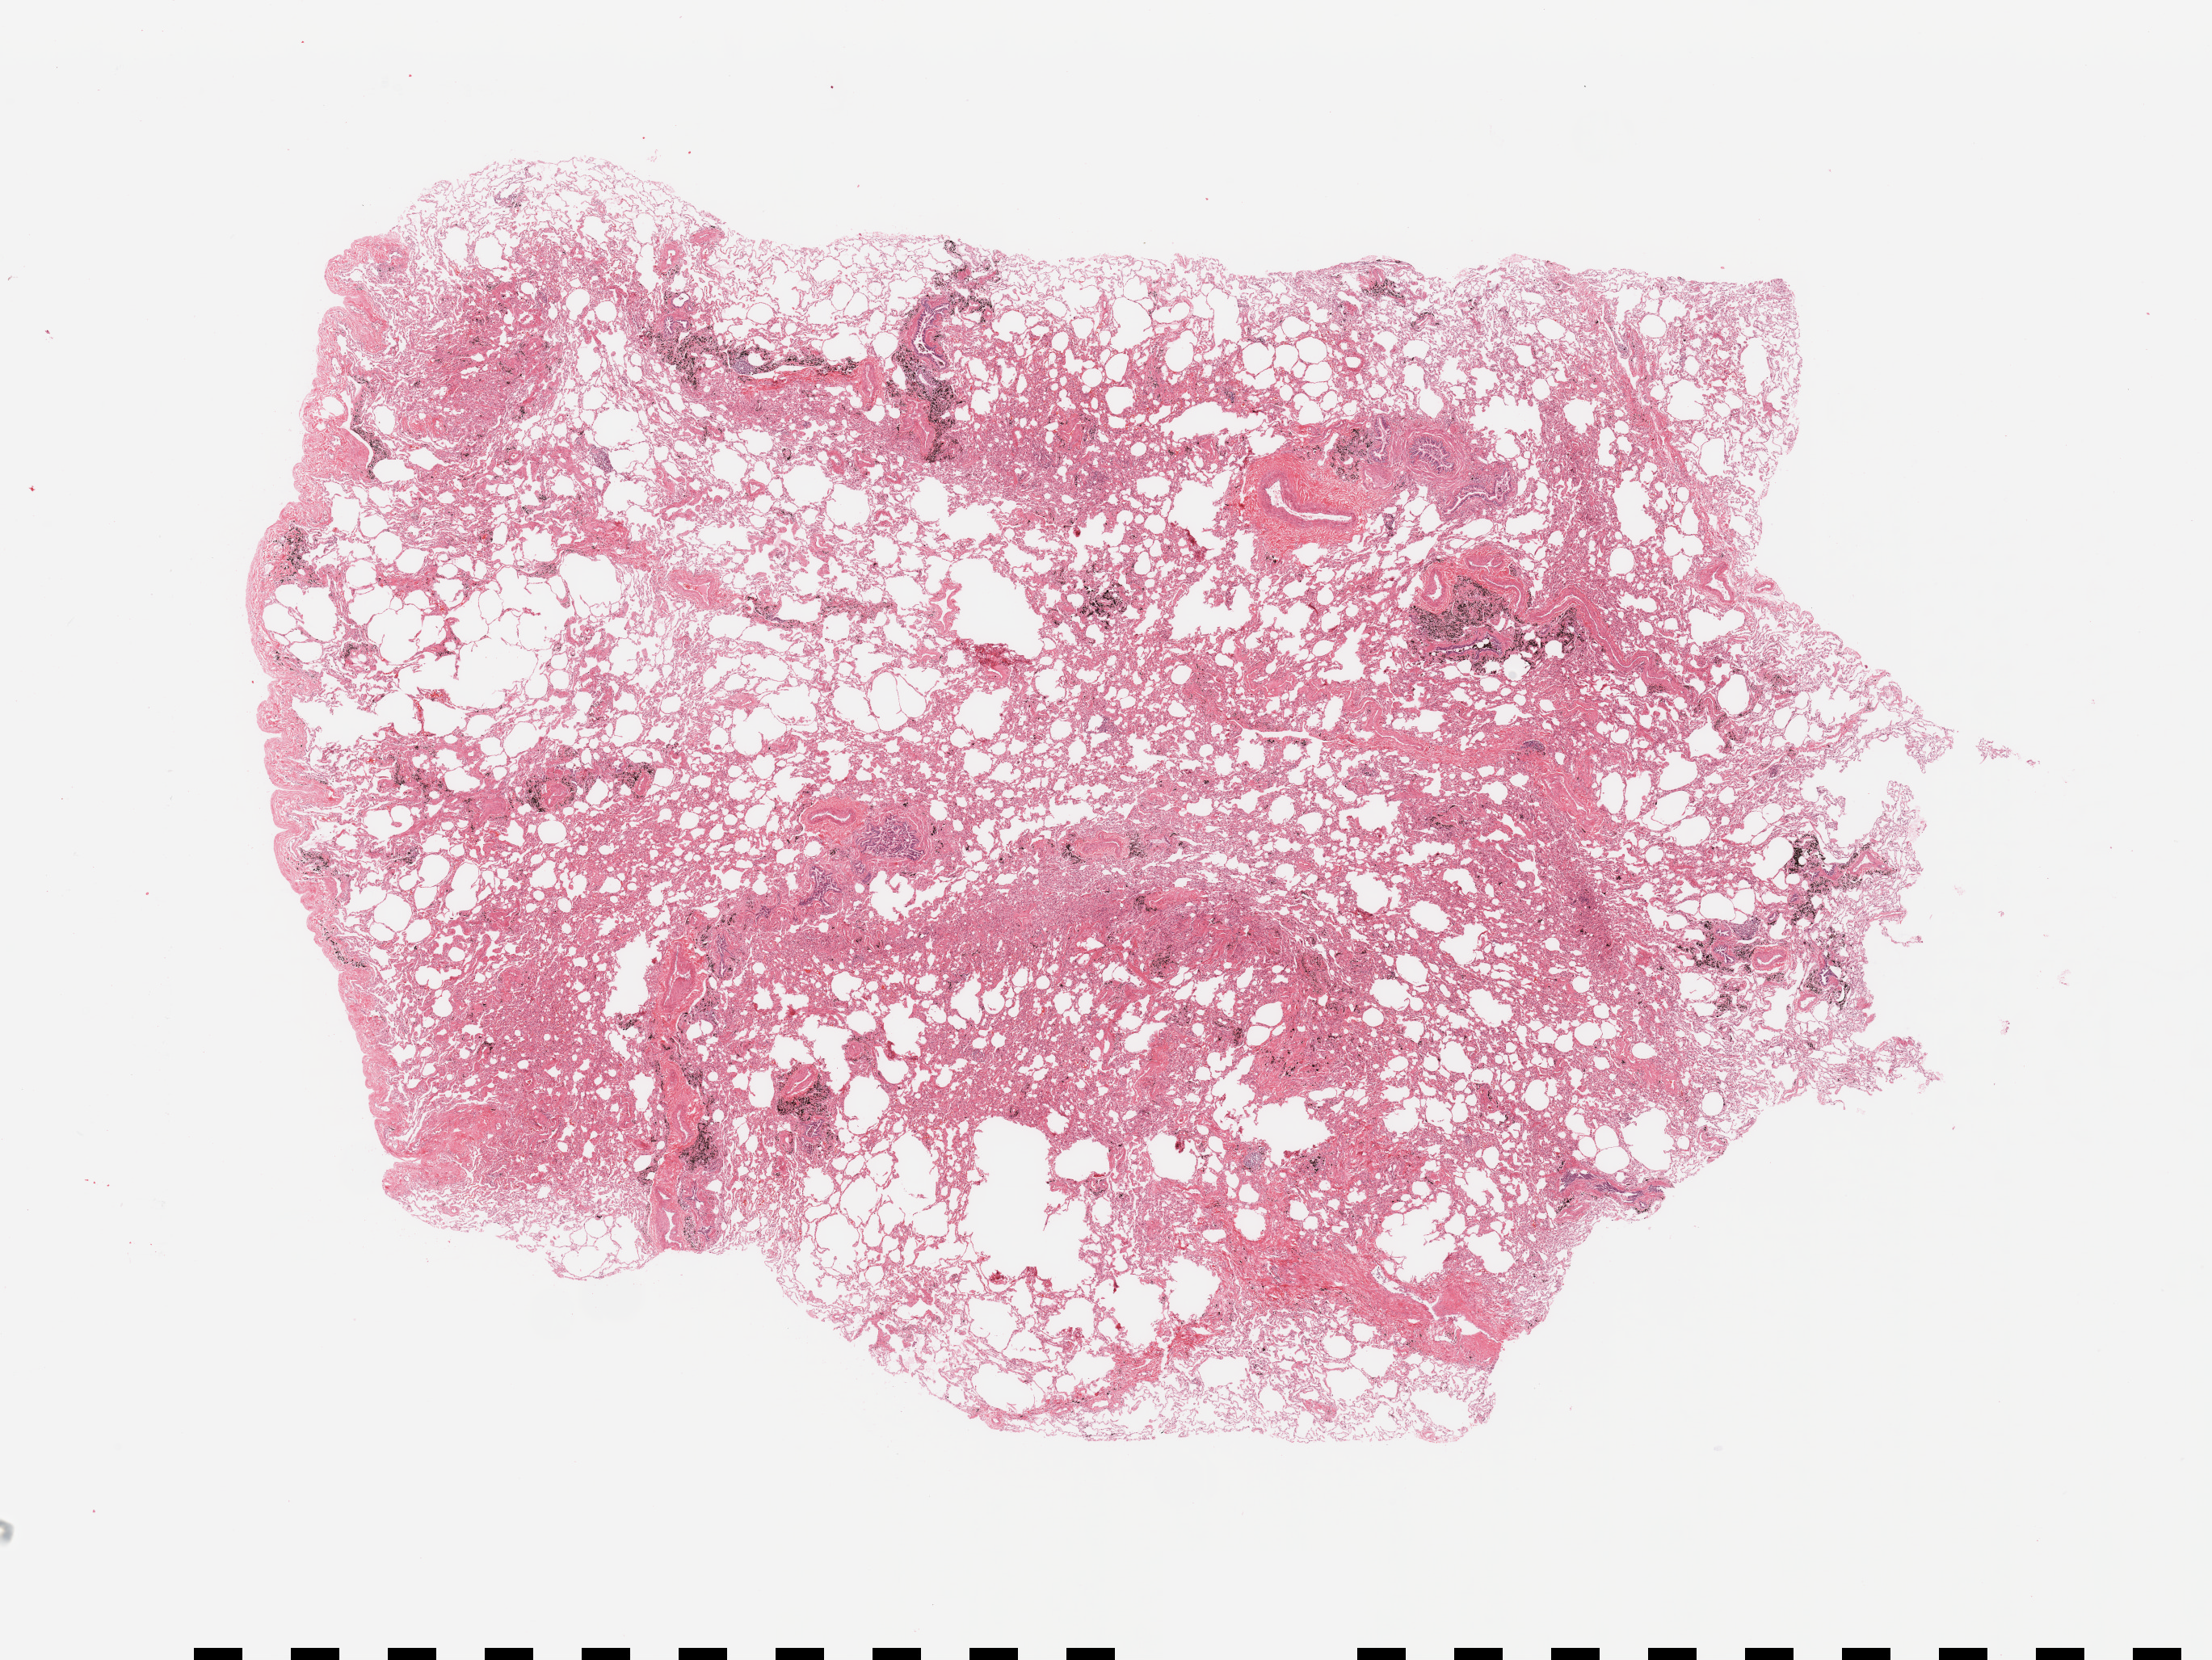
H&E whole-slide image — low-resolution overview of the scanned area, about 21.7 x 16.3 mm. Normal (non-tumour) tissue sample, sampled site: lung. Female, 55 y/o.
This section: normal (non-tumour) tissue from the same patient. Patient diagnosis: Adenocarcinoma, NOS.